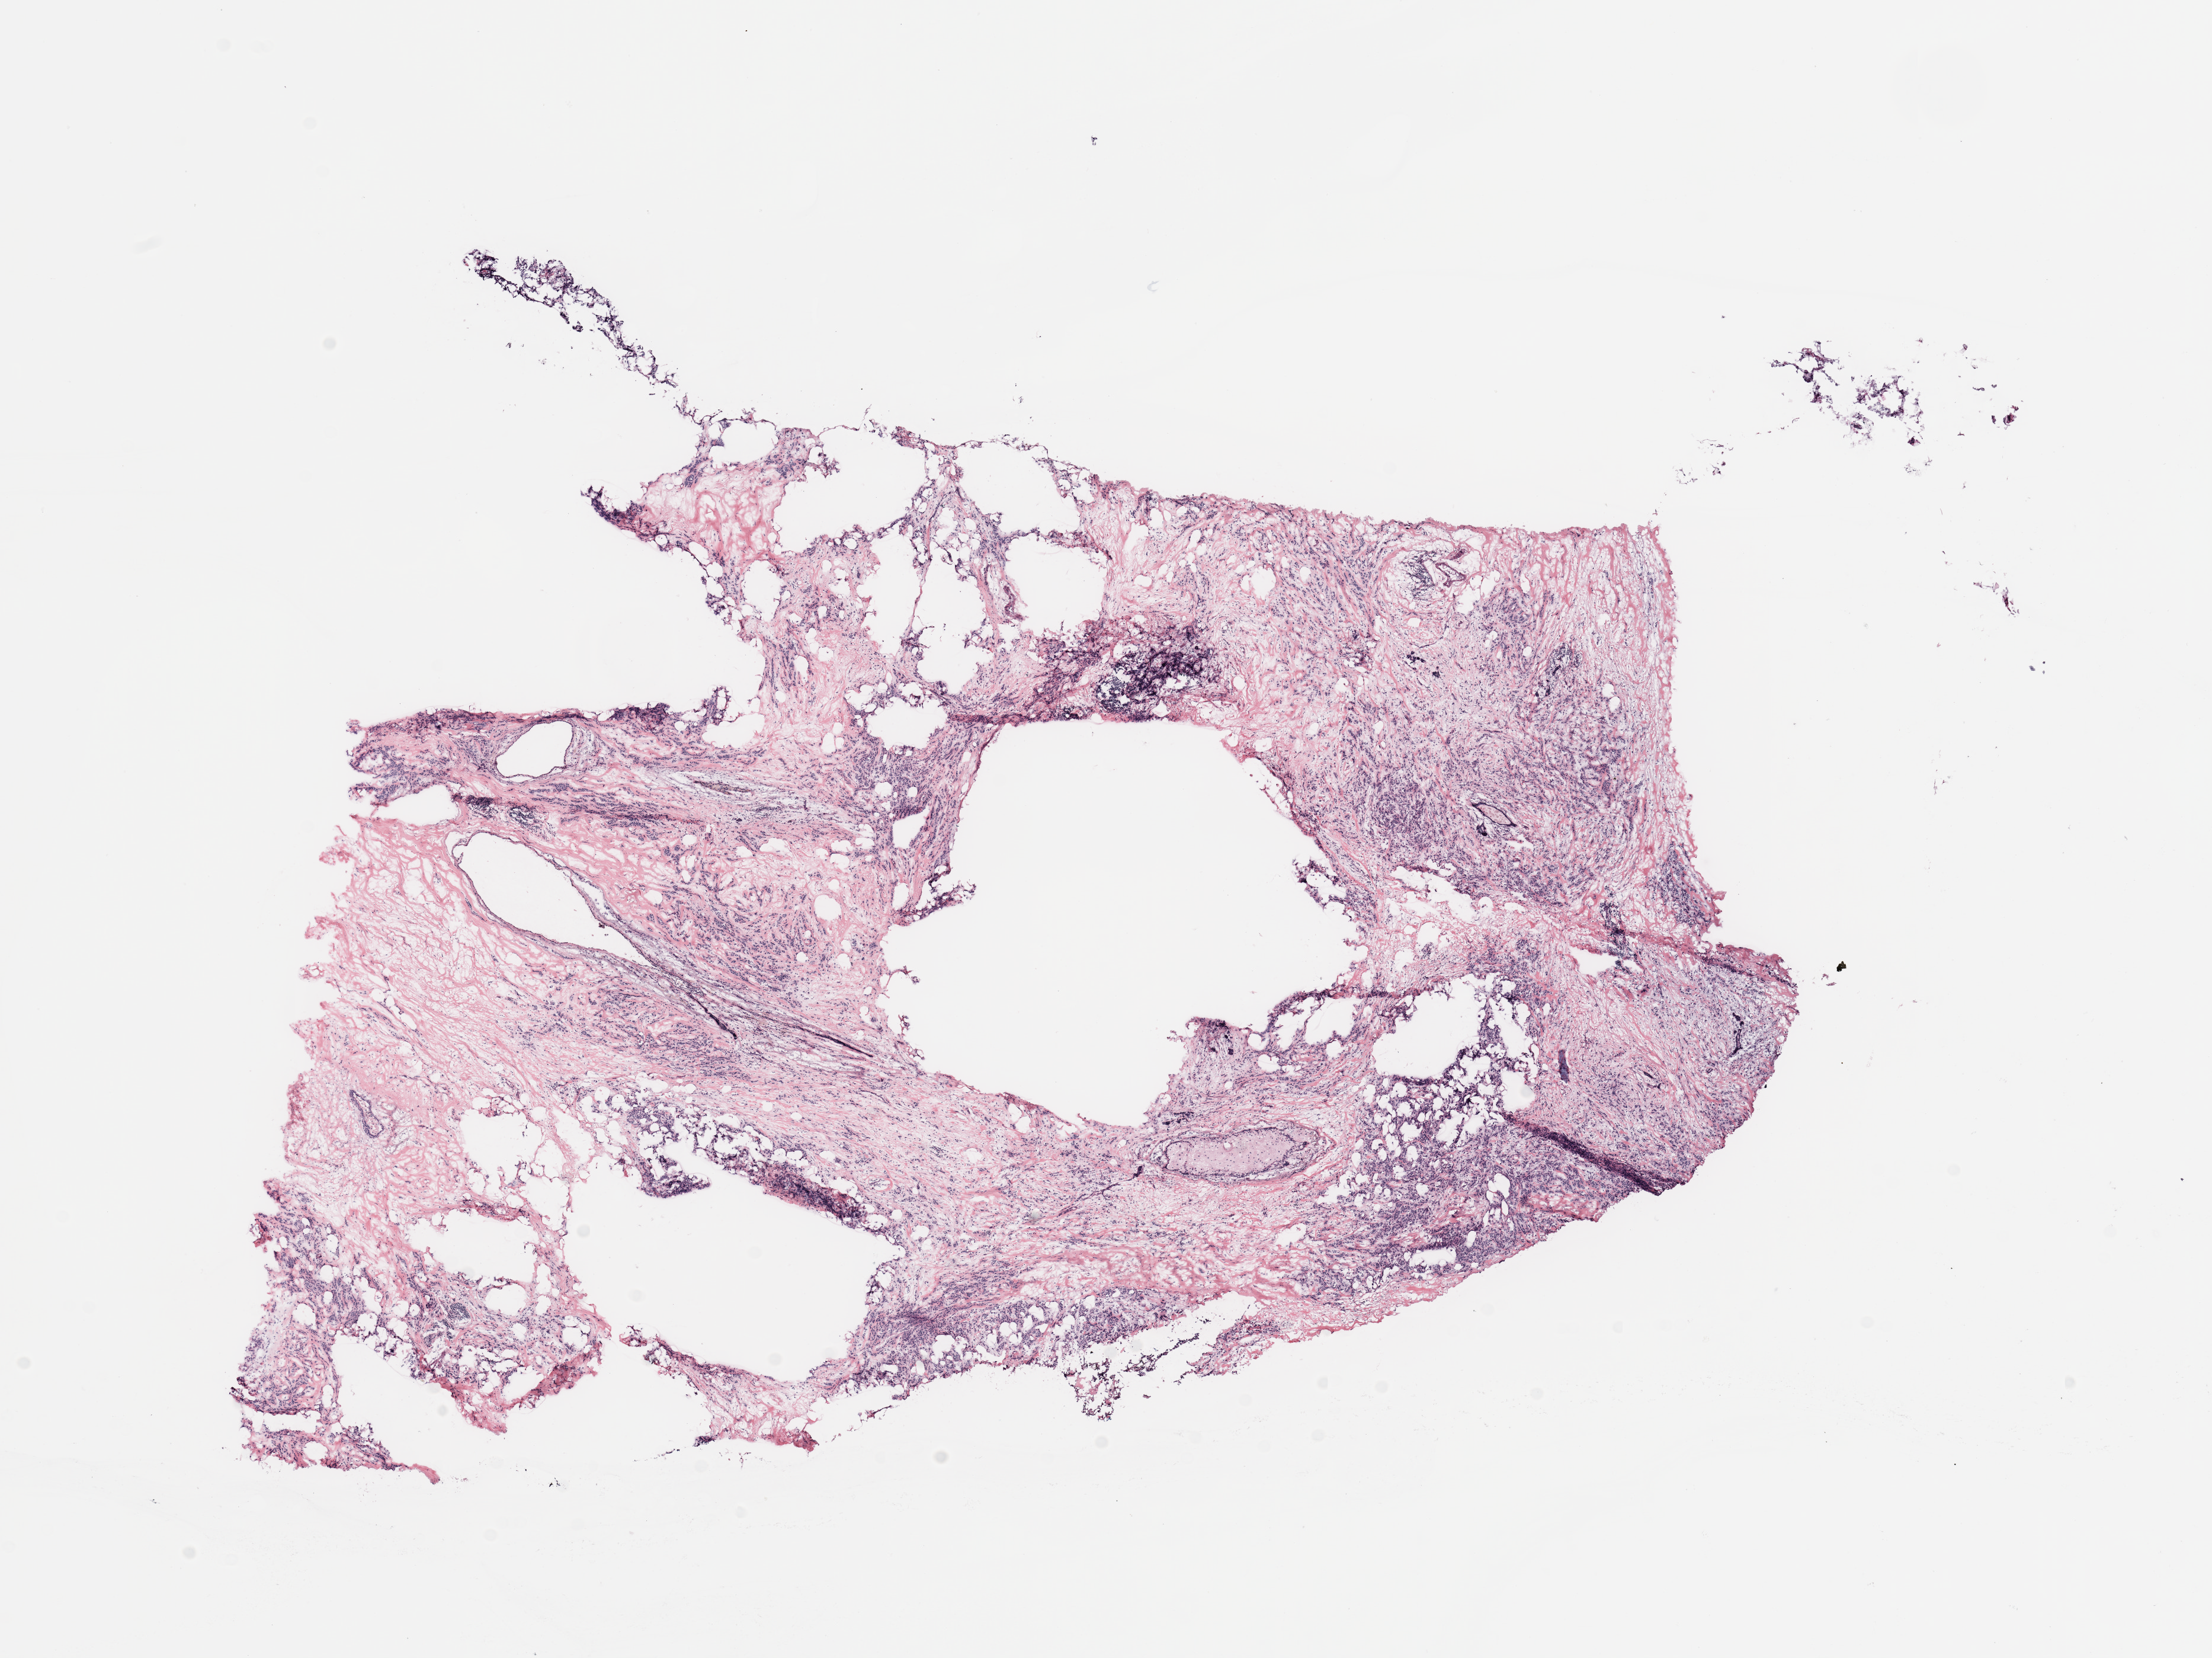
Digitized H&E-stained tissue section (whole slide) — whole scanned area (about 14.8 x 11.1 mm) shown as a low-resolution overview, breast, tissue type not recorded.
Patient diagnosis (cohort enrolment): breast cancer (breast).